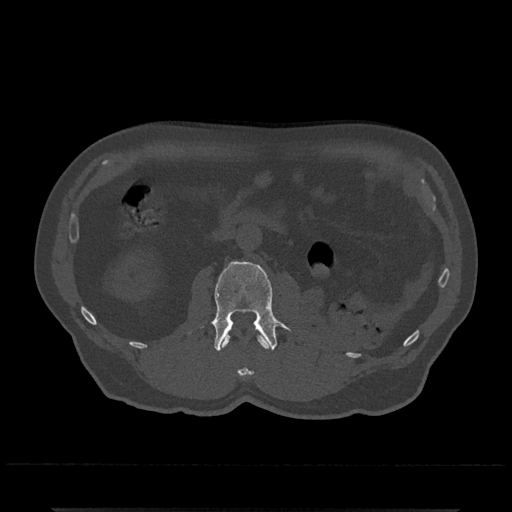
CT including the spine, one axial slice. Position 306 of 797 along the scan axis. Reconstruction kernel Br40s/3. 120 kVp. Bone window (W 1800 / L 400 HU). 512 × 512 image matrix, field of view 393 × 393 mm. Patient: male, 67 years. From the clinical record (not read from this slice): primary cancer: prostate.
Structures marked on this image (semi-automatic segmentation, software-assisted and operator-edited):
- L1 vertebra: bounding box [x1, y1, x2, y2] px = [221, 334, 269, 376]
- L2 vertebra: [211, 261, 291, 351]